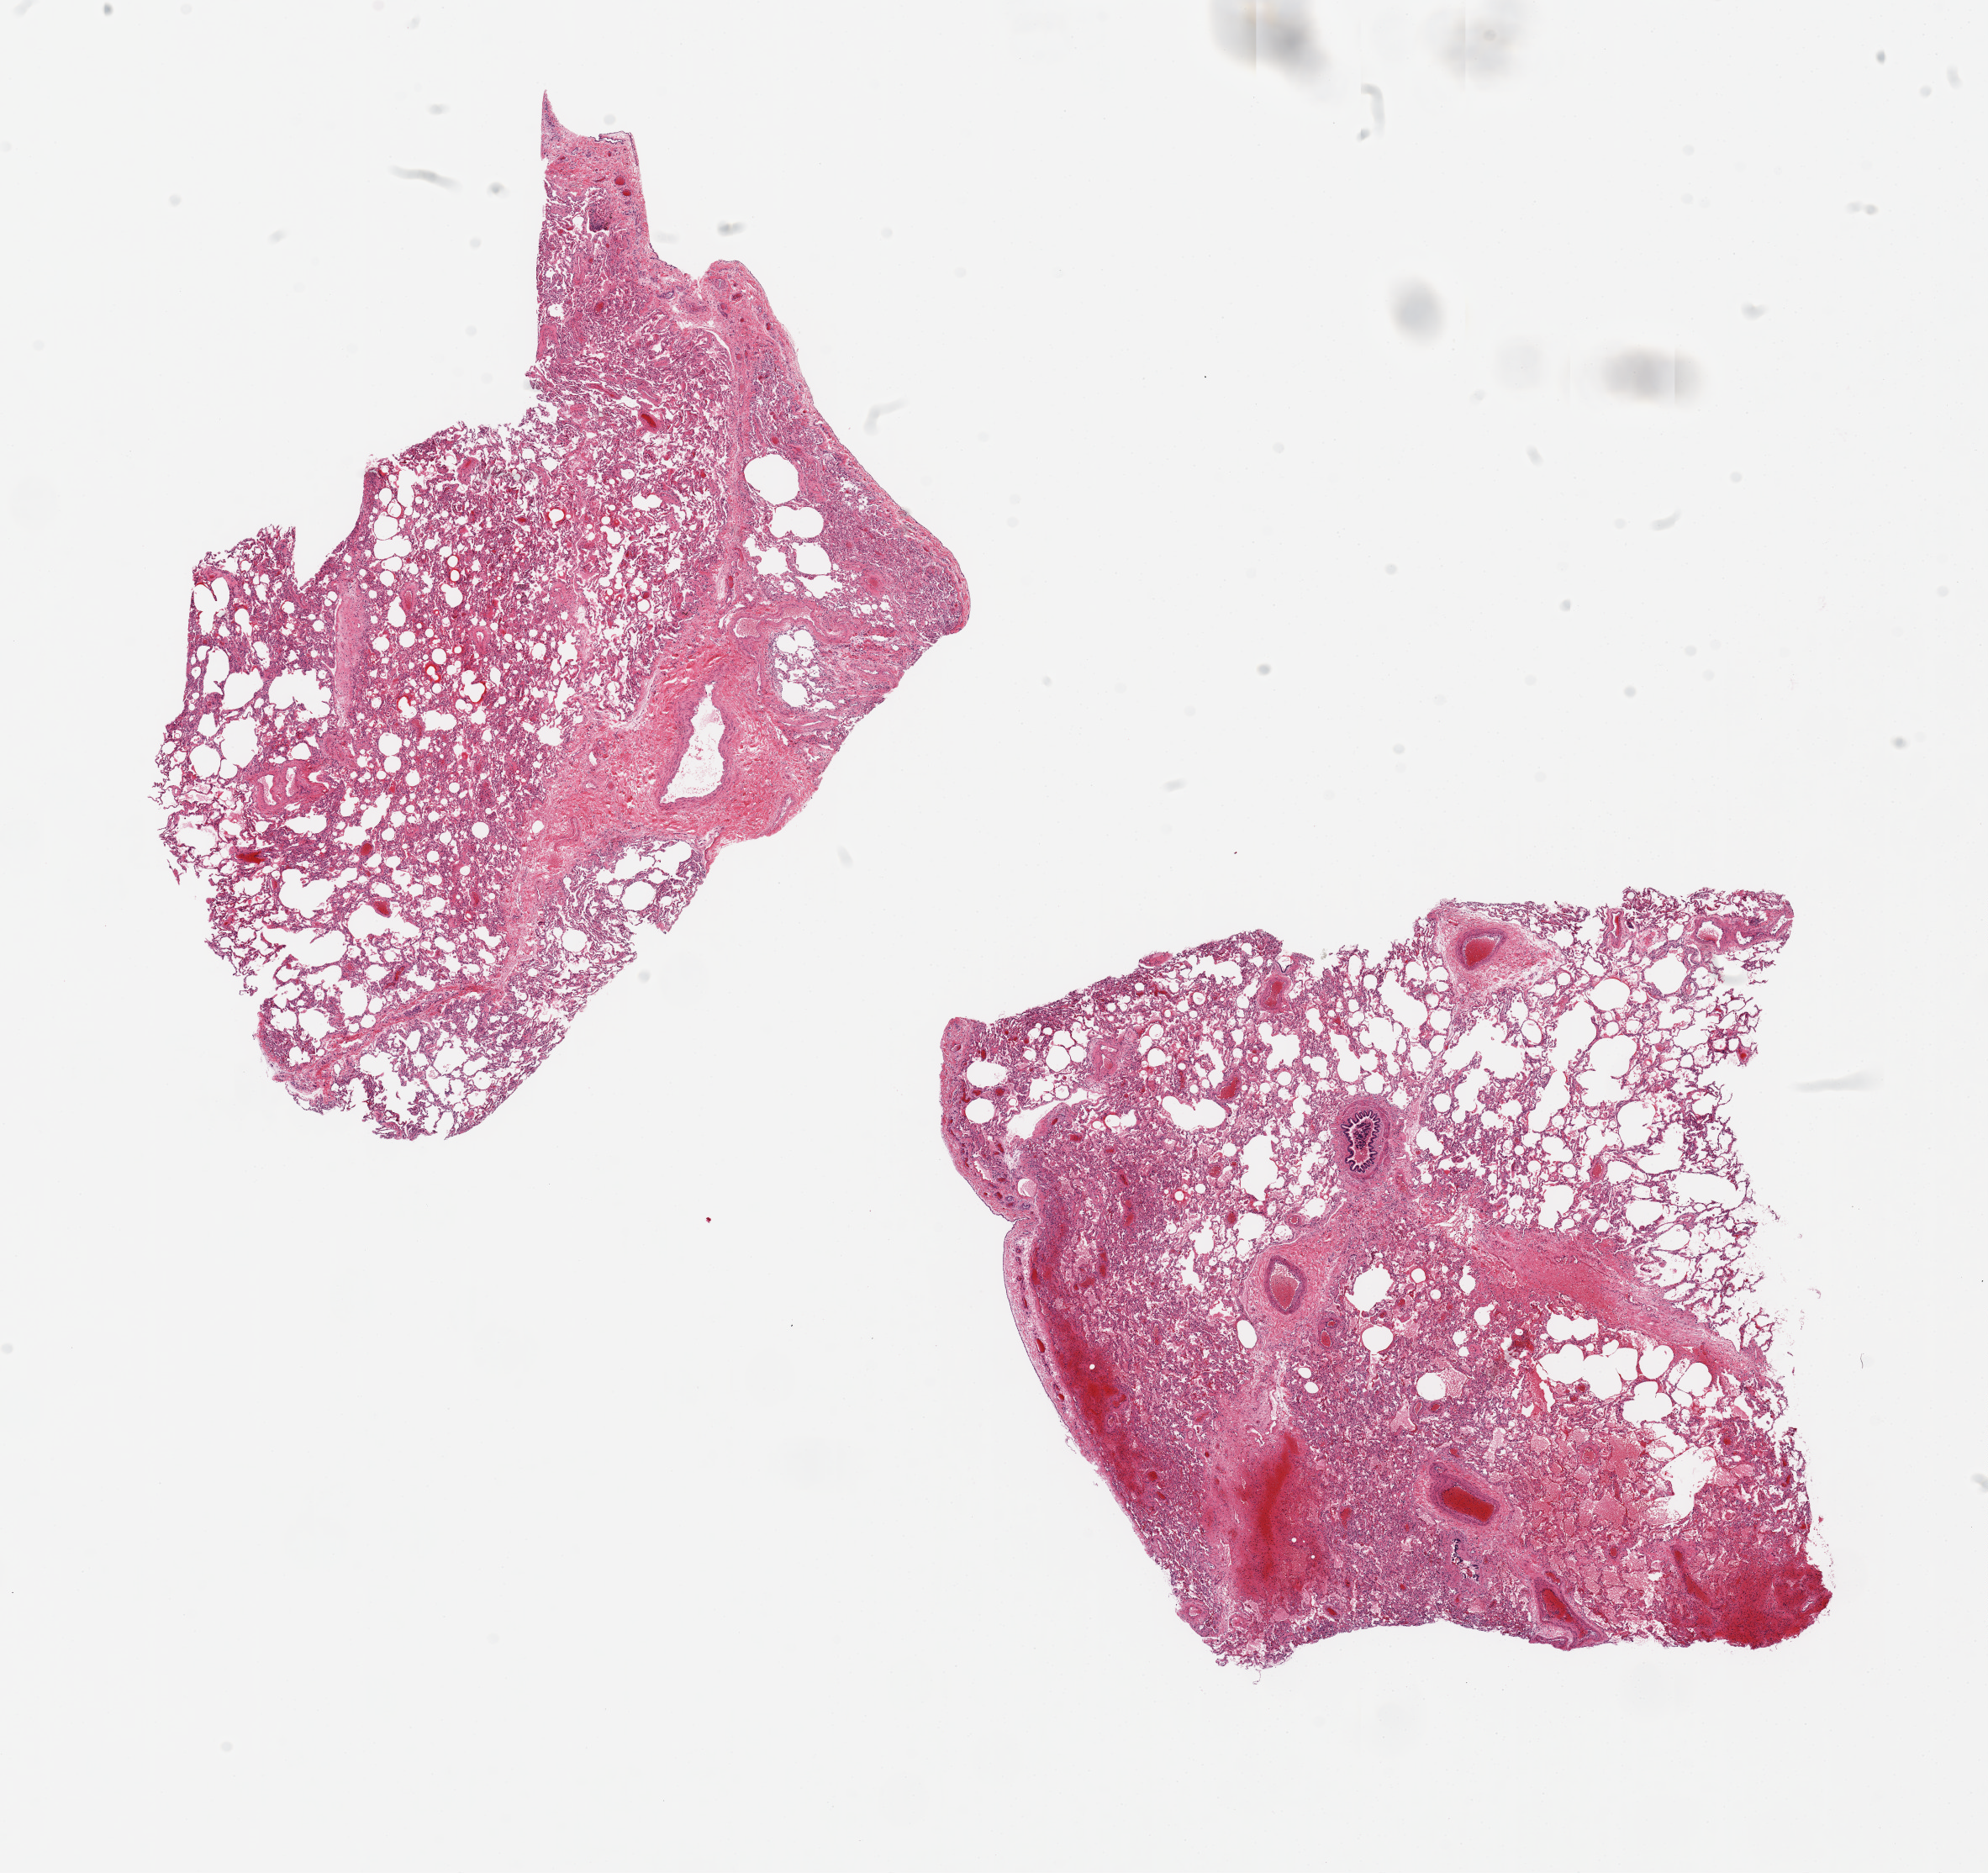
Digitized haematoxylin and eosin-stained section, brightfield — a low-resolution overview of the entire scanned area, about 18.7 x 17.6 mm (slide scanned at 20x), PAXgene-fixed paraffin-embedded (PFPE) section, sampled site (target tissue): lung, tissue donor sample. Male donor.
Pathologist's review note for this sample: 2 pieces, 8x7 & 10x7.5mm; scattered hemorrhages; pleura present (avoid).